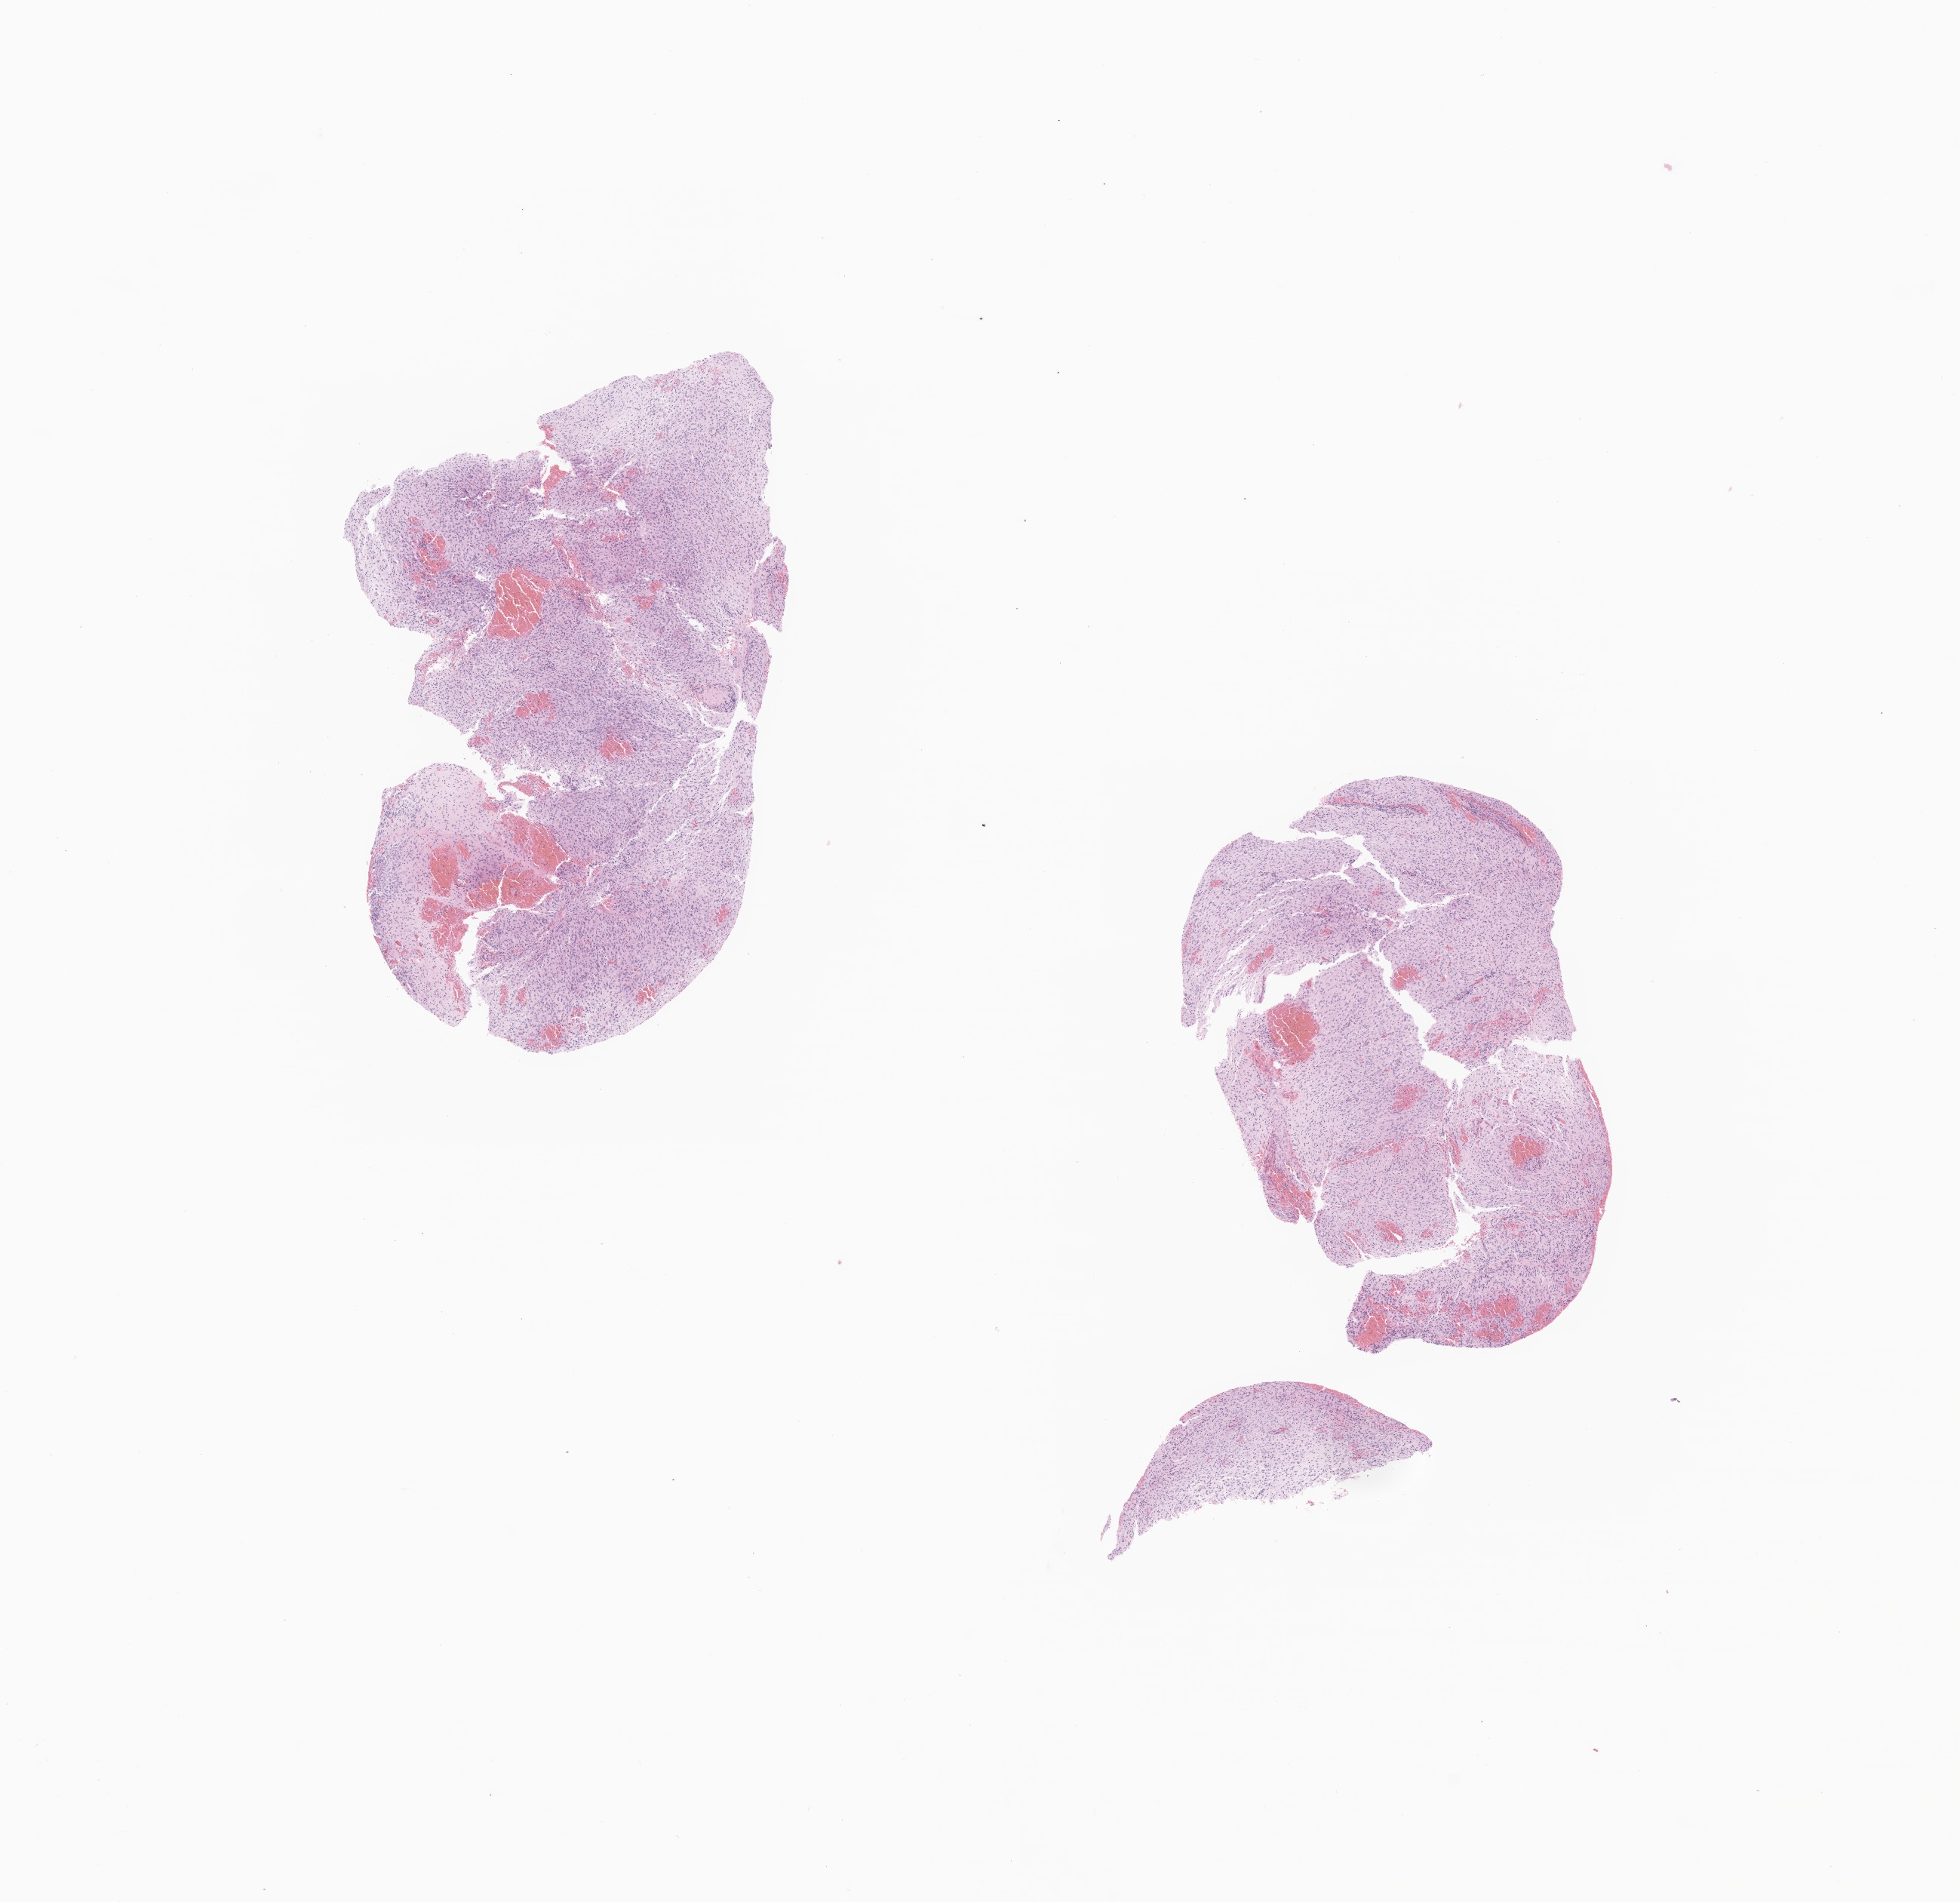
Digitized hematoxylin and eosin (H&E)-stained section of tumor tissue from the cerebellum — a low-resolution overview of the entire scanned area, about 11.0 x 10.6 mm. Formalin-fixed, paraffin-embedded (FFPE) tissue. Patient: male, age 924 days (about 2.5 years).
Recorded diagnosis: Astrocytoma, NOS.